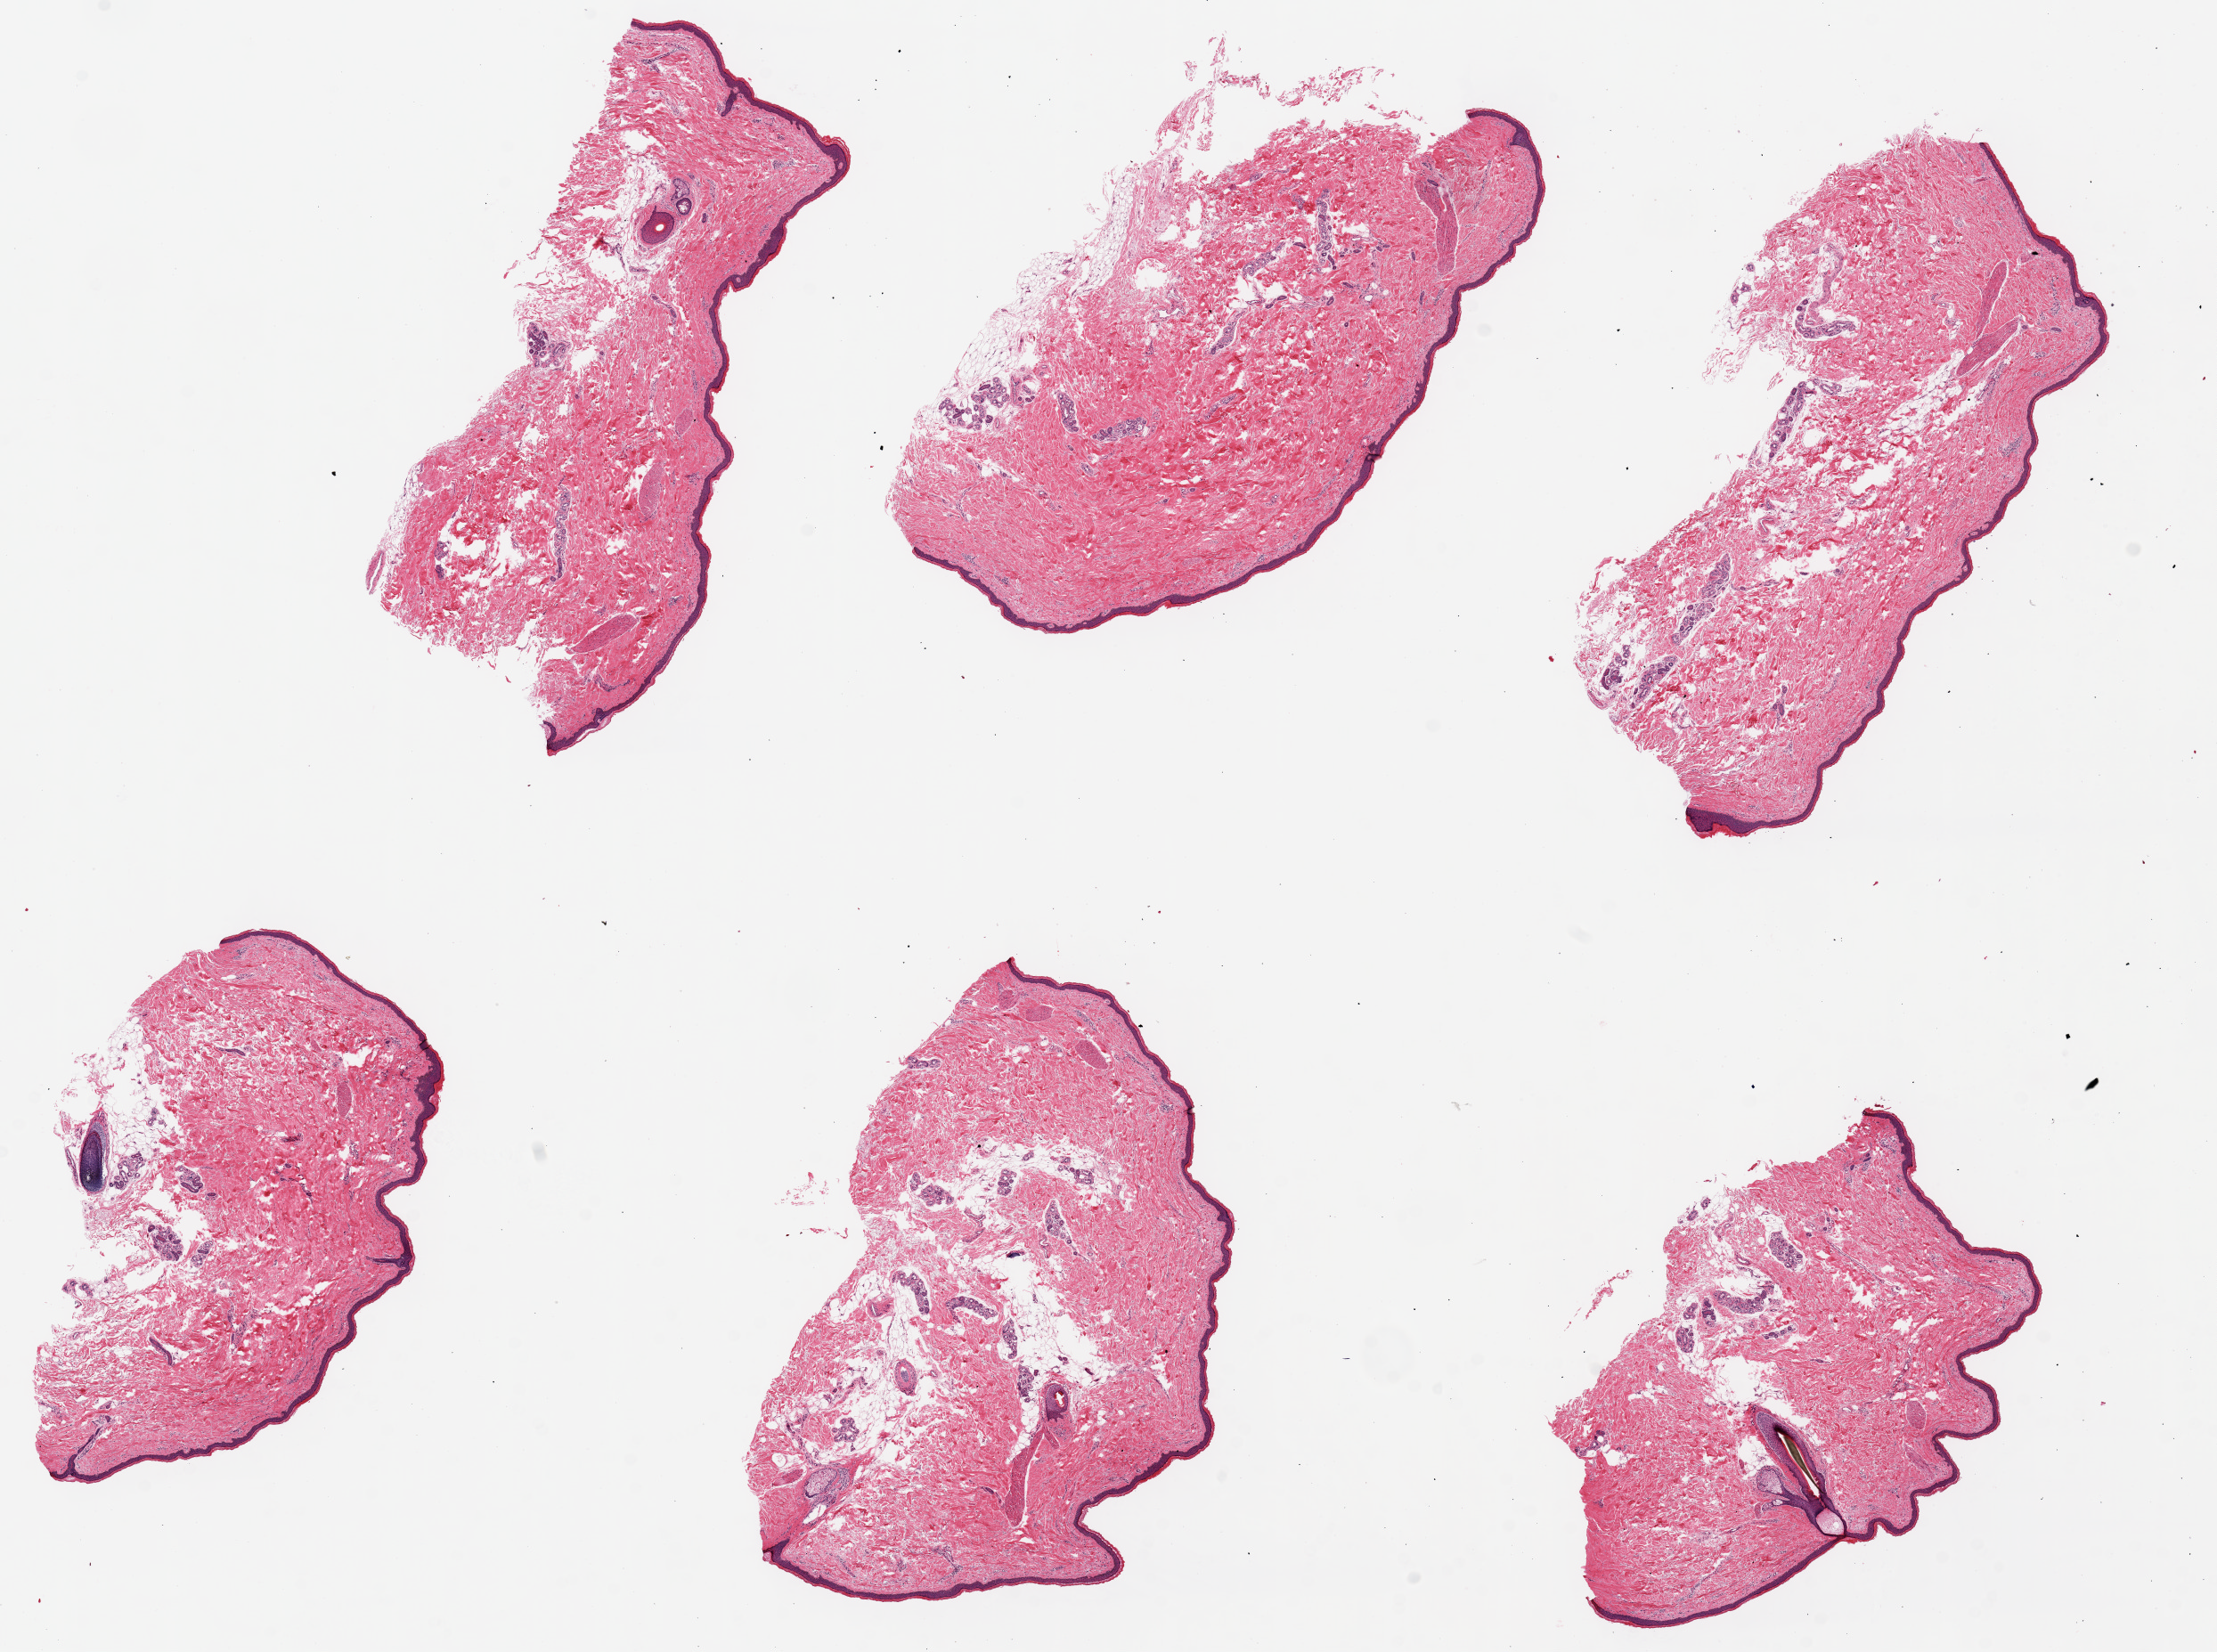
Whole-slide image, haematoxylin and eosin stain, brightfield — whole scanned area (about 19.7 x 14.7 mm) shown as a low-resolution overview; PAXgene-fixed paraffin-embedded (PFPE) section; target tissue: skin of lower leg; tissue donor sample. Donor: male.
* review note (as recorded): 6 pieces, up to 7x3mm; Subcutaneous adipose is well trimmed. Abundant sweat glands